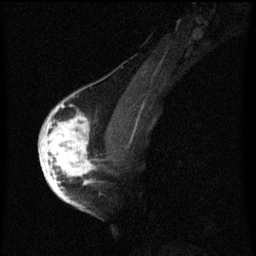
Breast MRI (dynamic contrast-enhanced), one sagittal slice. Slice 37 of 60 in the series (ordered by position). Dynamic contrast-enhanced series, image 2 of 3 at this slice position (ordered by acquisition). 1.5 T. TE 4.2 ms, TR 8 ms. 2 mm slice thickness. 256 × 256 image matrix, field of view 180 × 180 mm. Female patient, age 56 years.
Structures marked on this image (semi-automatic segmentation, software-assisted and operator-edited):
- analysis volume of interest (the breast-tissue region the enhancement analysis was run in; not a lesion): bounding box [x1, y1, x2, y2] px = [42, 110, 97, 193]
- tumour enhancement mask (voxels above the 70 % enhancement threshold inside the analysis volume of interest): [42, 110, 97, 193]